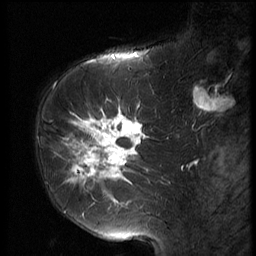
Breast MRI (dynamic contrast-enhanced), one sagittal slice; position 23 of 56 along the scan axis; 3 images stored at this slice position (order not interpretable as contrast timing); 1.5 T; TE 4.2 ms, TR 9 ms; 256 × 256 image matrix. Female patient, age 61 years. From the clinical record (not read from this slice): setting: breast cancer imaged before/during neoadjuvant chemotherapy; receptor status: HR-positive, HER2-negative.
Outlined on this slice (semi-automatically segmented with operator editing):
- analysis volume of interest (the breast-tissue region the enhancement analysis was run in; not a lesion): box from (x=47, y=89) to (x=153, y=191) px
- tumour enhancement mask (voxels above the 140 % enhancement threshold inside the analysis volume of interest): (x=54, y=114)–(x=147, y=183)